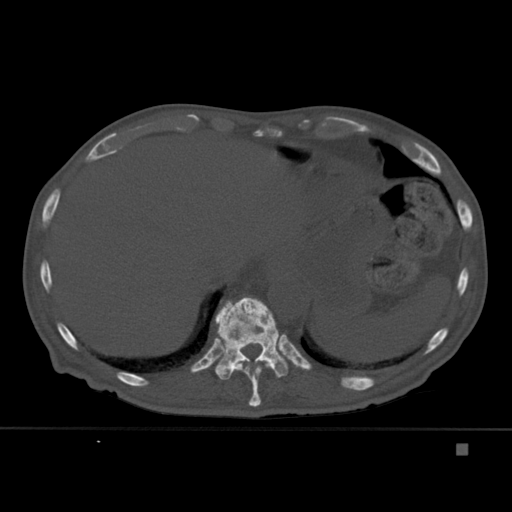
CT including the spine, one axial slice; bone window (W 1800 / L 400 HU); 512 × 512 image matrix, field of view 378 × 378 mm. Patient: male, 75 years. From the clinical record (not read from this slice): primary cancer: prostate.
Outlined on this slice (semi-automatically segmented with operator editing):
- T10 vertebra: bounding box <231,363,278,407> (left, top, right, bottom; pixels)
- T11 vertebra: <214,297,288,380>